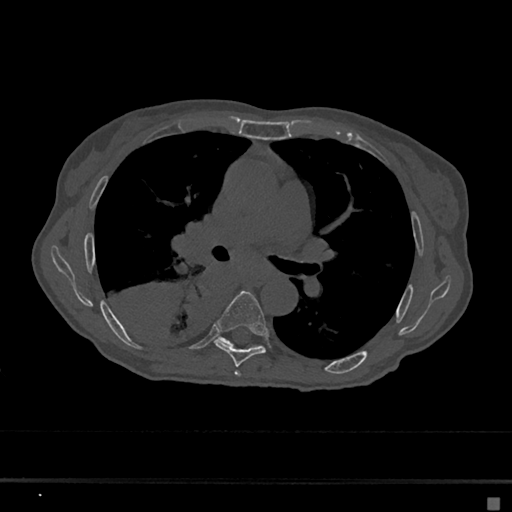
CT including the spine, one axial slice; slice 409 of 797 in the series (ordered by position); bone window (W 1800 / L 400 HU); 0.5 mm slice thickness; 512 × 512 image matrix, field of view 360 × 360 mm. Patient: female, 68 years. Case-level facts recorded for this patient, not image findings: primary cancer: renal.
Structures marked on this image (semi-automatic segmentation, software-assisted and operator-edited):
- T5 vertebra: box from (x=235, y=371) to (x=241, y=377) px
- T6 vertebra: (x=214, y=291)–(x=268, y=367)
- T7 vertebra: (x=220, y=337)–(x=258, y=348)